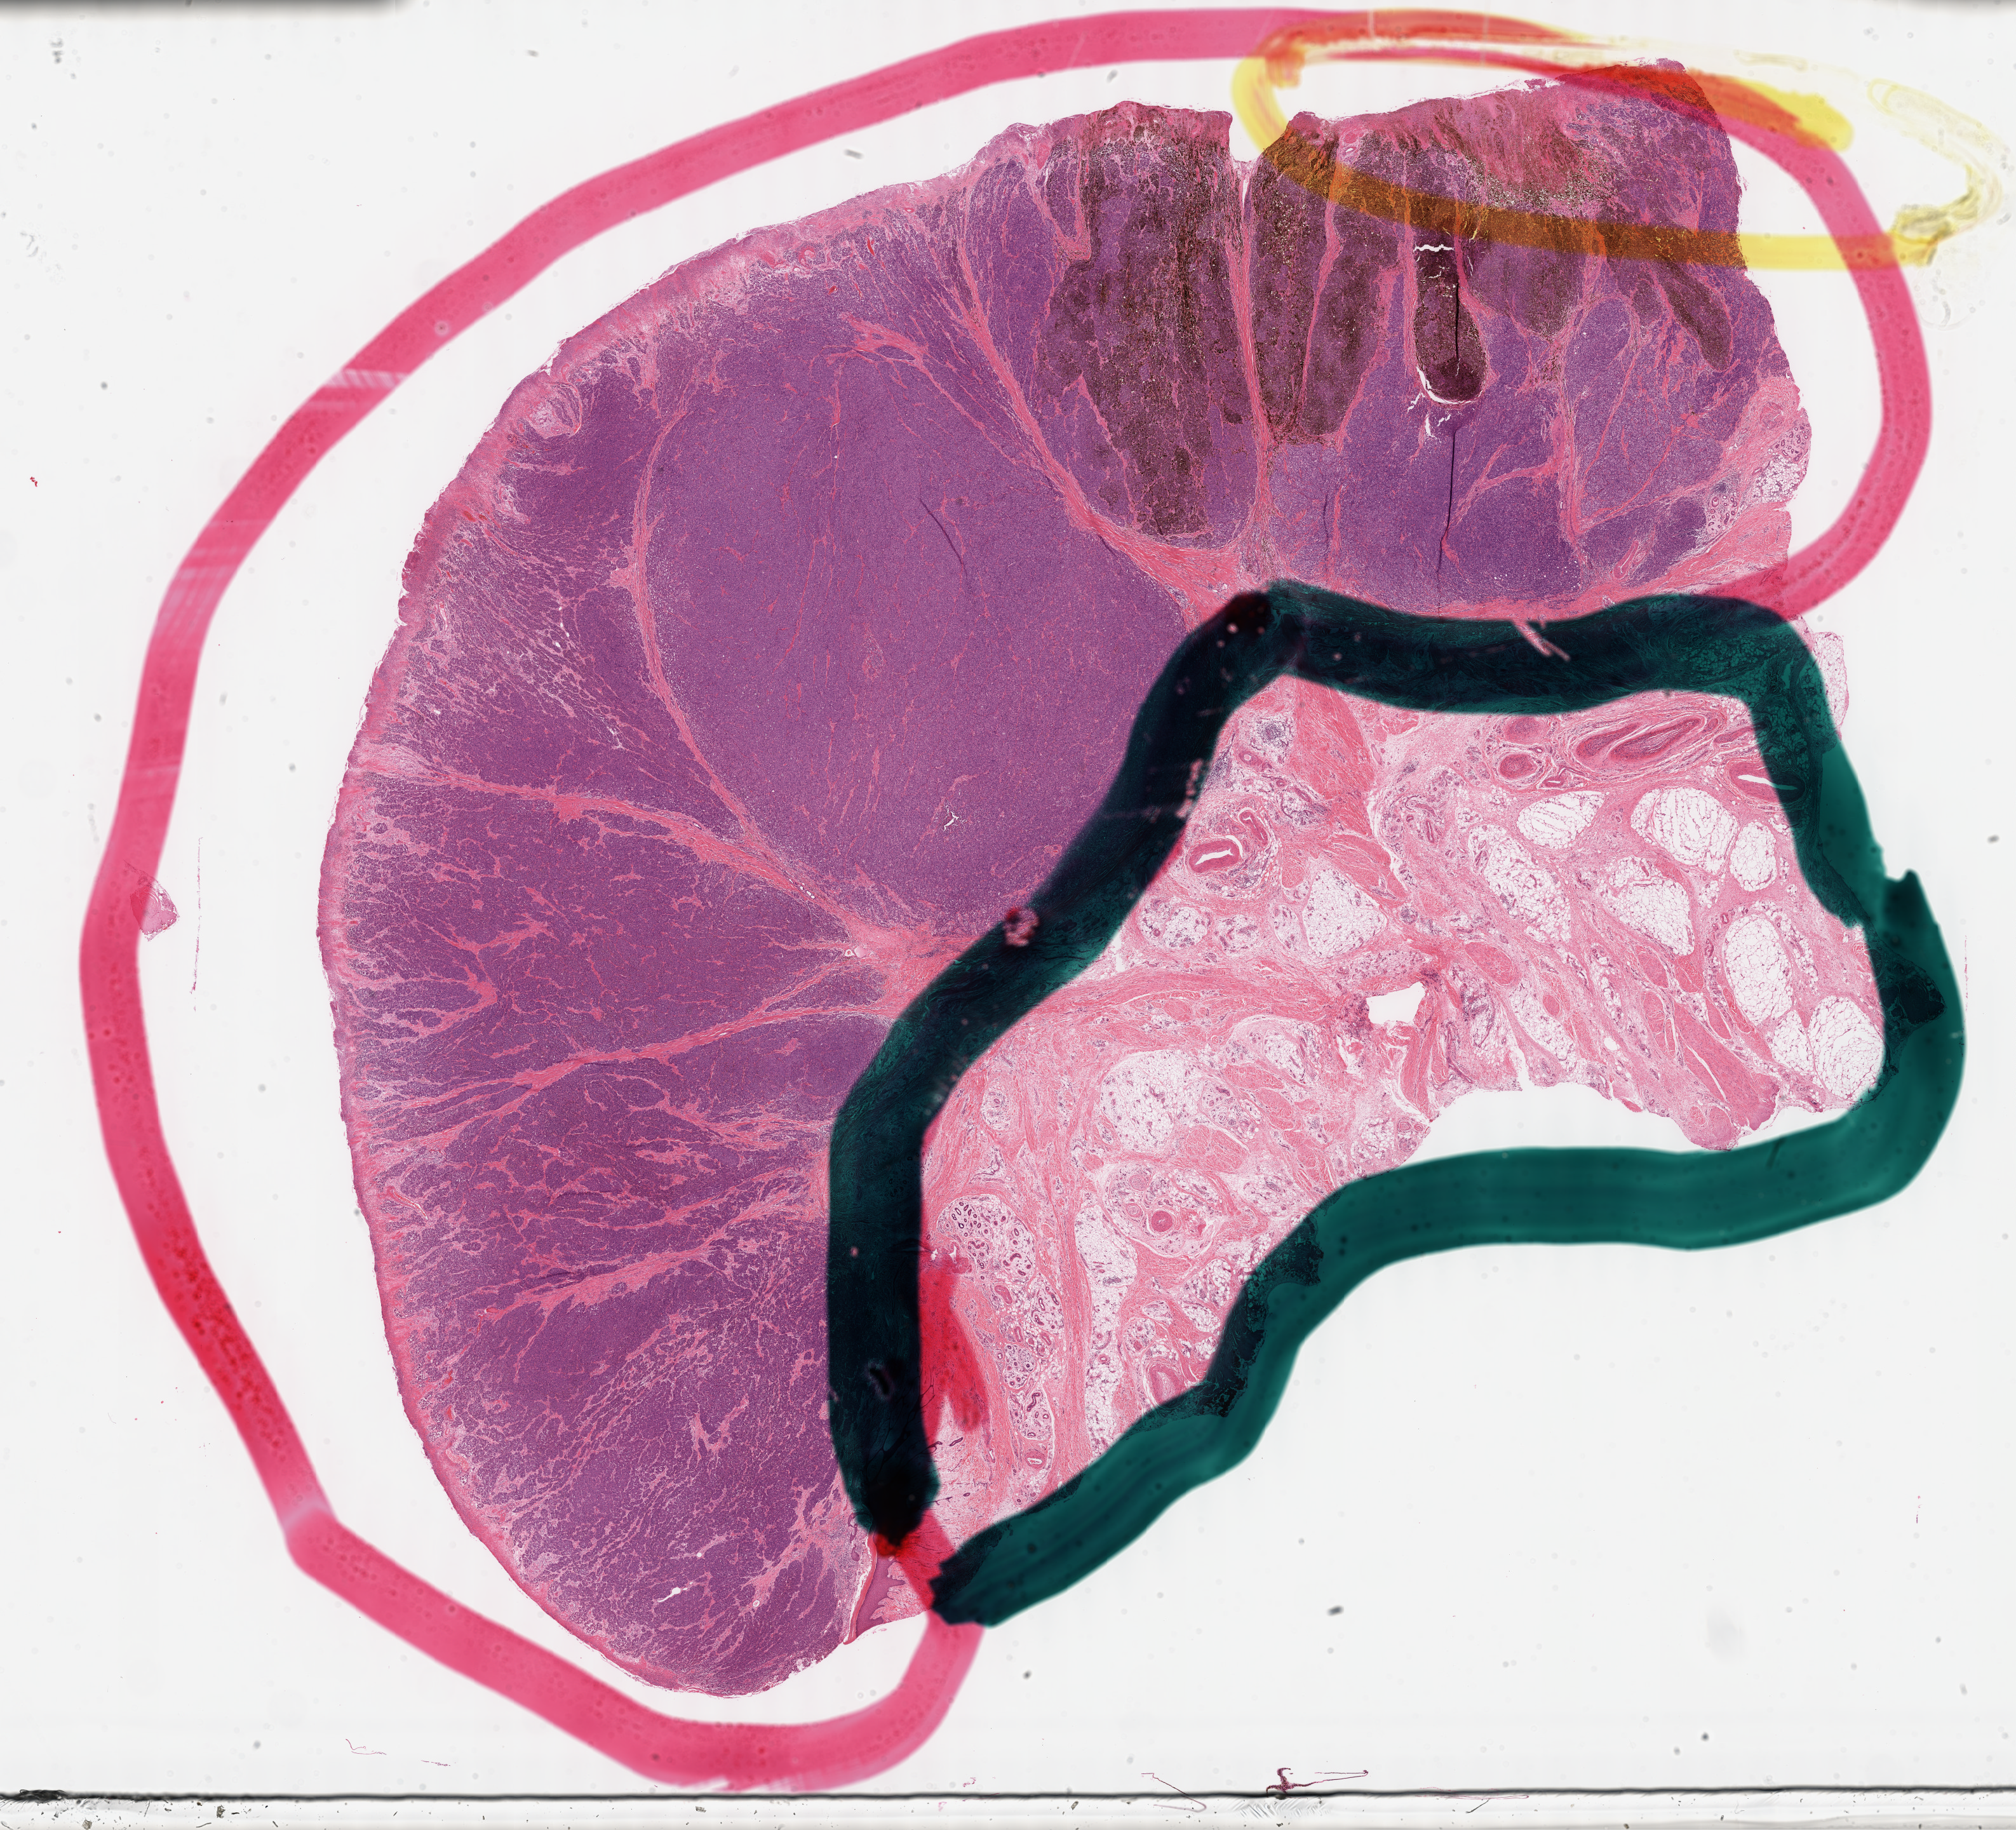
Digitized H&E tissue section (whole slide), low-resolution overview of the scanned area, about 25.7 x 23.3 mm, formalin-fixed paraffin-embedded (FFPE) diagnostic section, skin, primary tumour sample. Patient: female, age at initial diagnosis 70 years.
Pathologic diagnosis: Malignant melanoma, NOS.